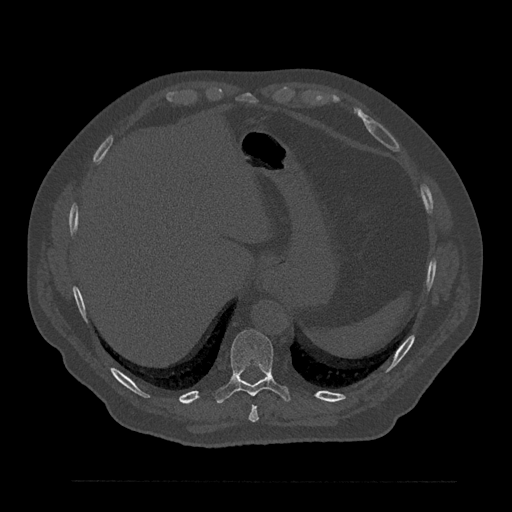
CT including the spine, one axial slice. Slice 354 of 797 in the series (ordered by position). 120 kVp. Bone window (W 1800 / L 400 HU). 512 × 512 image matrix, field of view 430 × 430 mm. Patient: male, 61 years. Case-level facts recorded for this patient, not image findings: primary cancer: prostate.
Outlined on this slice (semi-automatic segmentation, software-assisted and operator-edited):
- T10 vertebra: box from (x=215, y=329) to (x=291, y=403) px
- T9 vertebra: (x=248, y=405)–(x=259, y=422)